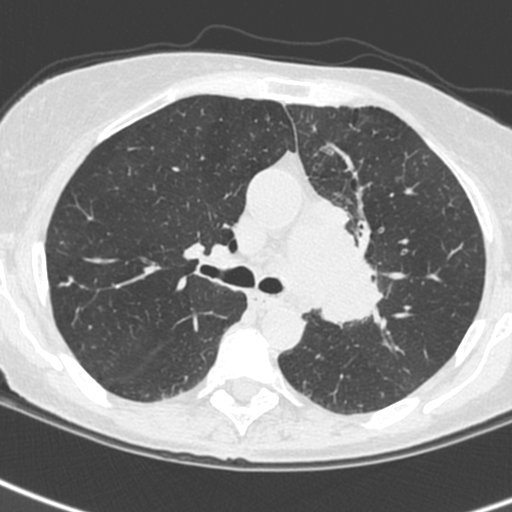
Low-dose screening chest CT, one axial slice; position 159 of 242 along the scan axis; 120 kVp; lung window (W 1500 / L -600 HU); 1.3 mm slice thickness; 512 × 512 image matrix.
Structures marked on this image (outlined manually by an expert reader):
- lesion 3 (tumor, upper lobe of left lung): box from (x=312, y=197) to (x=383, y=324) px